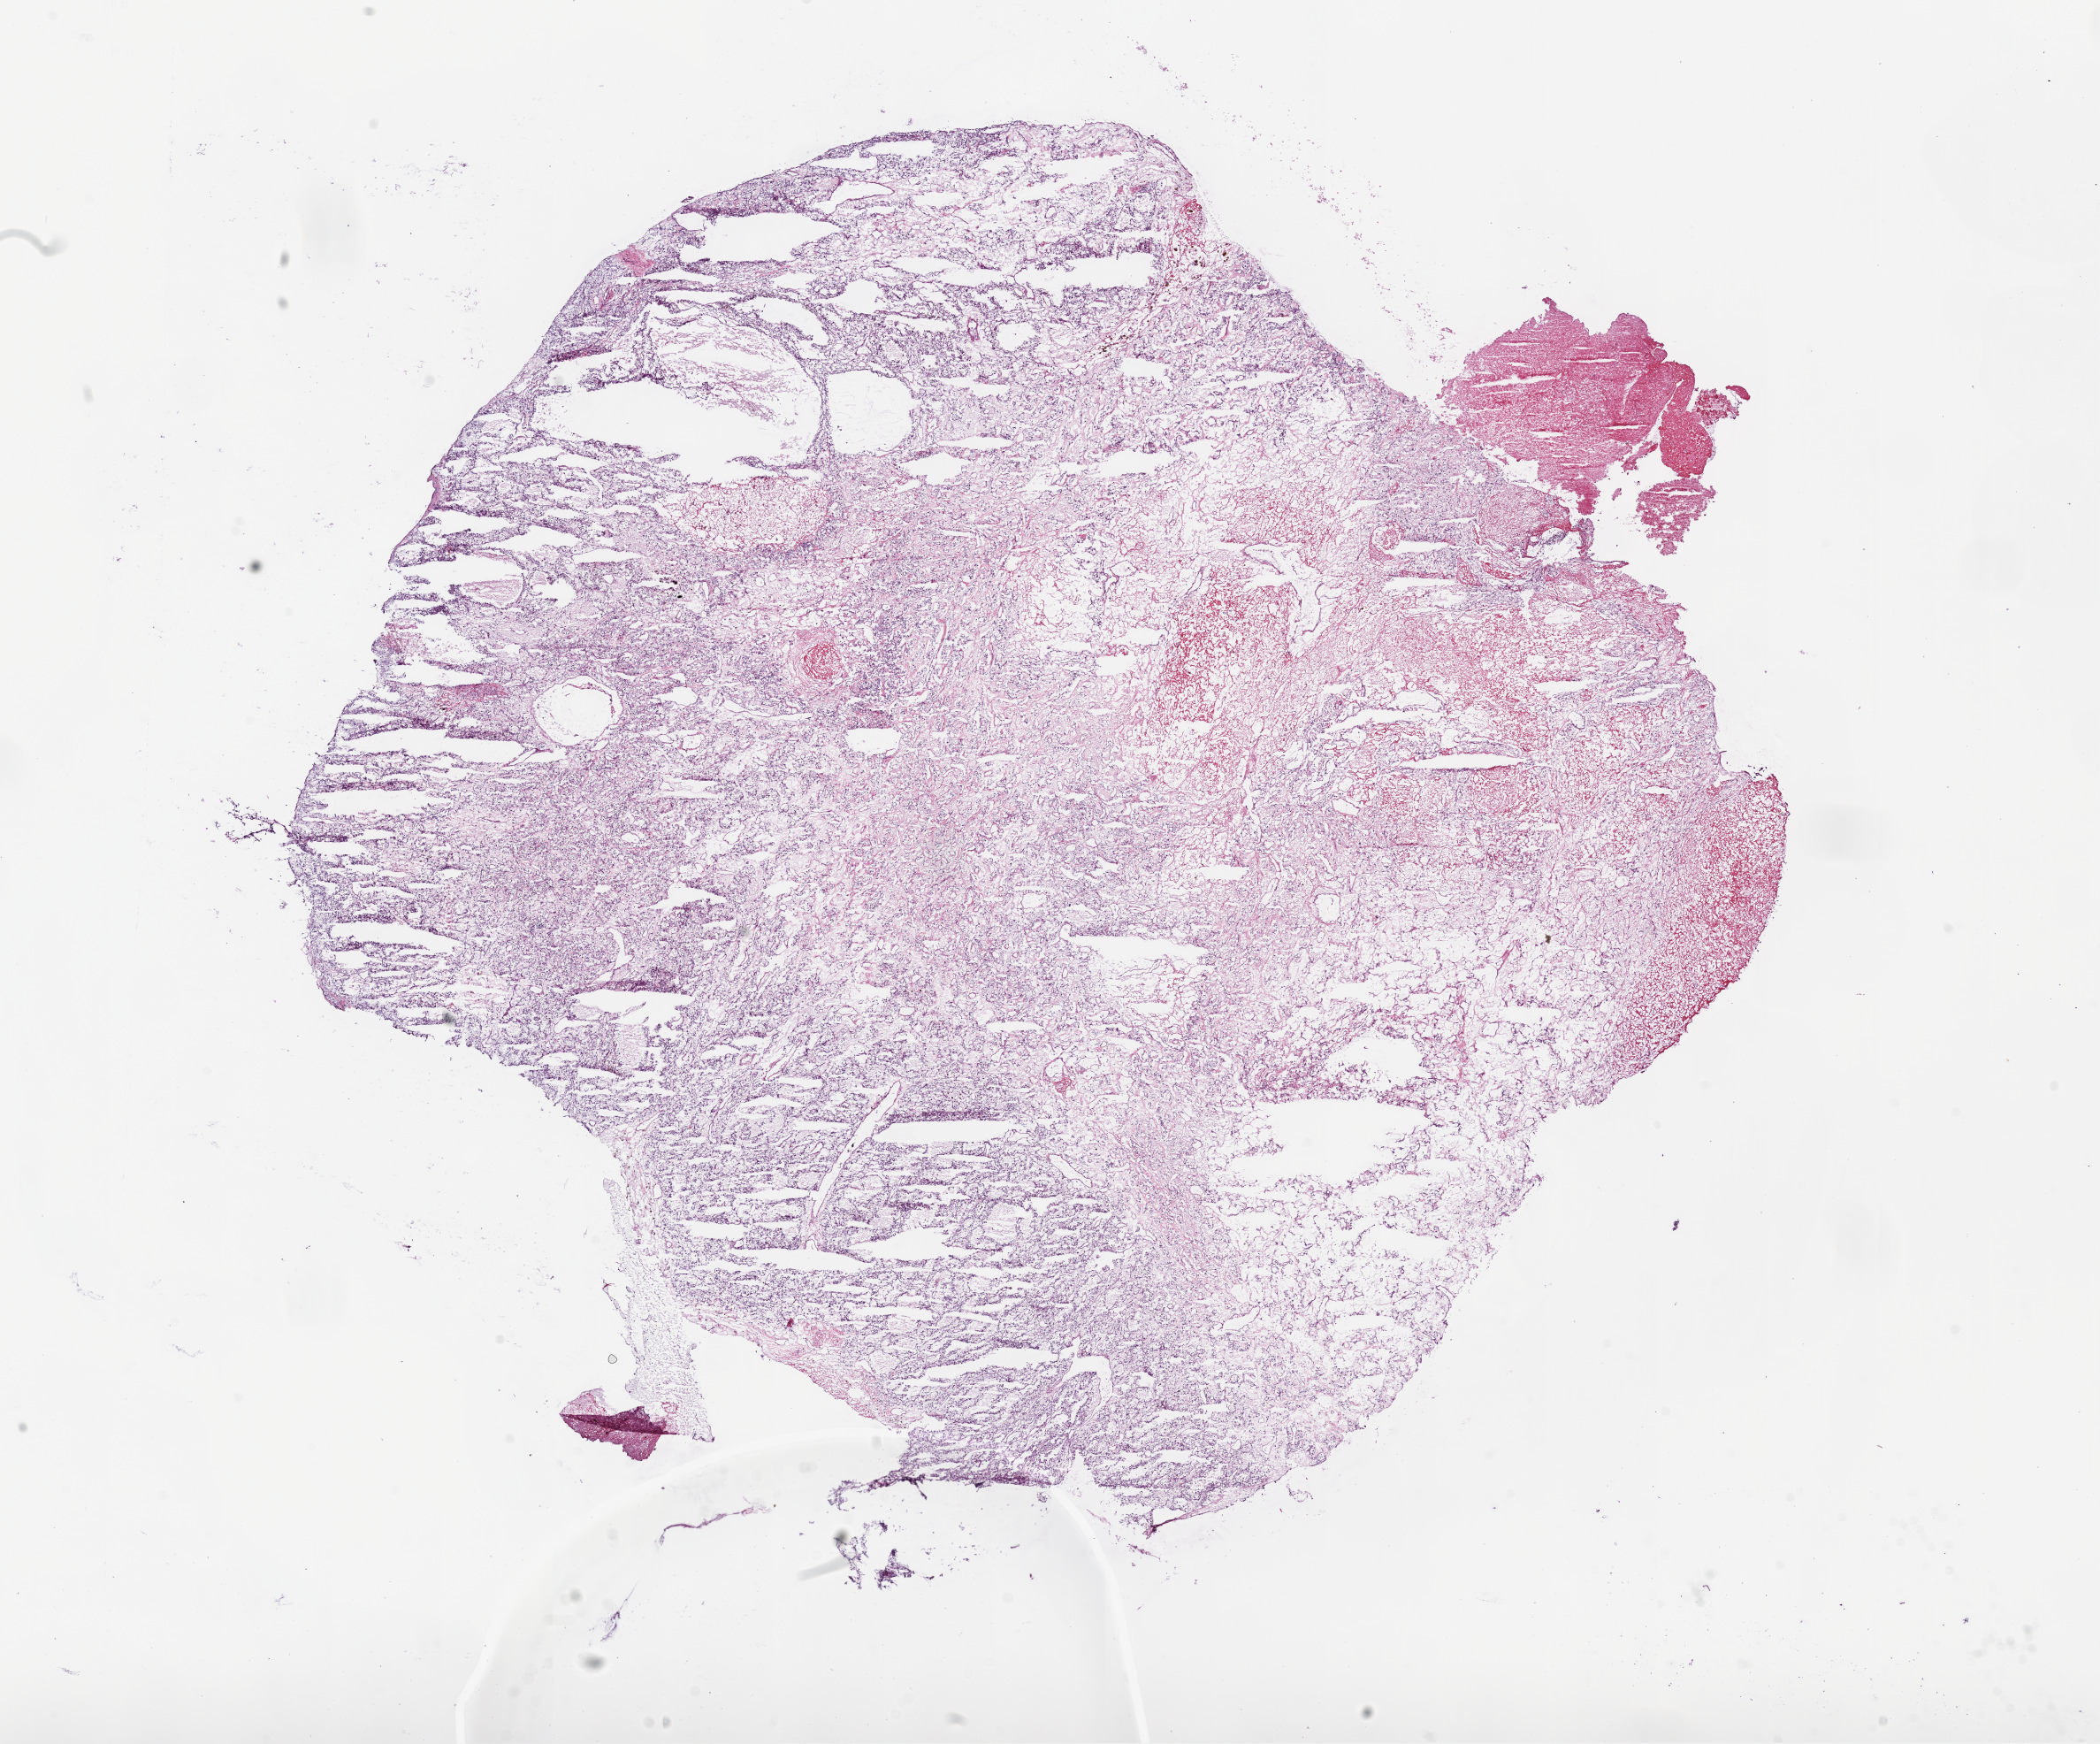
Digitized H&E tissue section (whole slide) — a low-resolution overview of the entire scanned area, about 19.1 x 15.8 mm (slide scanned at 20x); frozen section; primary tumour sample from the kidney. Male, age 61 years at initial diagnosis. Histologic grade: G2 (moderately differentiated). Composition of this section per pathologist review: tumour cells 73%, tumour nuclei 80%, normal cells 0%, stromal cells 25%, necrosis 2%.
Diagnosis: Clear cell adenocarcinoma, NOS. AJCC pathologic stage: I.